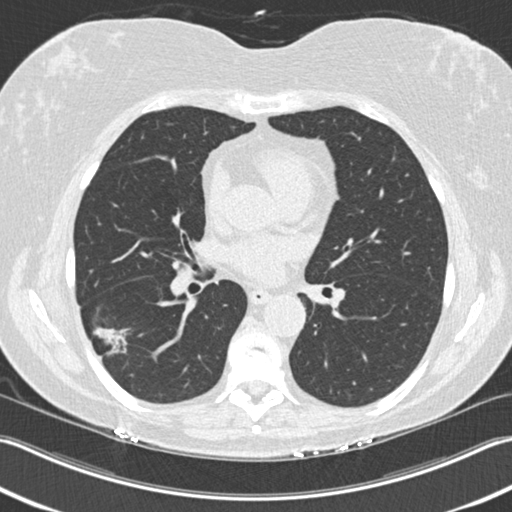
Axial slice from a low-dose chest CT screening exam, baseline annual screen, lung window (W 1500 / L -600 HU), standard (soft-tissue) reconstruction kernel (B30f), 512 × 512 image matrix, field of view 348 × 348 mm. Female, age 63 years at enrolment. Current smoker at enrolment.
Lesion marked by an expert reader, bounding box <81,317,142,372> (left, top, right, bottom; pixels). The screening reader recorded 3 non-calcified nodules or masses ≥4 mm on this exam (right upper lobe, right lower lobe, right lower lobe); which of them this box marks is not recorded. Official screen result: positive, change unspecified: nodule(s) >= 4 mm or enlarging nodule(s), mass(es), or other non-specific abnormalities suspicious for lung cancer. Later outcome: lung cancer diagnosed 57 days after this screen — bronchiolo-alveolar adenocarcinoma, NOS, right lower lobe, well differentiated (G1), stage IA (AJCC 6th edition), 25 mm at pathology.